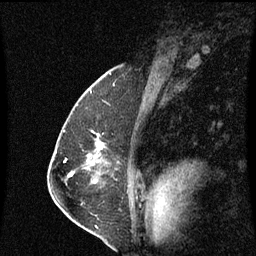
Breast MRI (dynamic contrast-enhanced), one sagittal slice; slice 41 of 60 in the series (ordered by position); dynamic contrast-enhanced series, image 2 of 3 at this slice position (ordered by acquisition); 1.5 T; TE 4.2 ms, TR 8.9 ms; 256 × 256 image matrix, field of view 200 × 200 mm. Female patient, age 57 years. Case-level facts recorded for this patient, not image findings: setting: breast cancer imaged before/during neoadjuvant chemotherapy; receptor status: HR-positive, HER2-negative.
Structures marked on this image (semi-automatic segmentation, software-assisted and operator-edited):
- analysis volume of interest (the breast-tissue region the enhancement analysis was run in; not a lesion): bounding box [x1, y1, x2, y2] px = [85, 136, 102, 159]
- tumour enhancement mask (voxels above the 70 % enhancement threshold inside the analysis volume of interest): [97, 144, 102, 149]